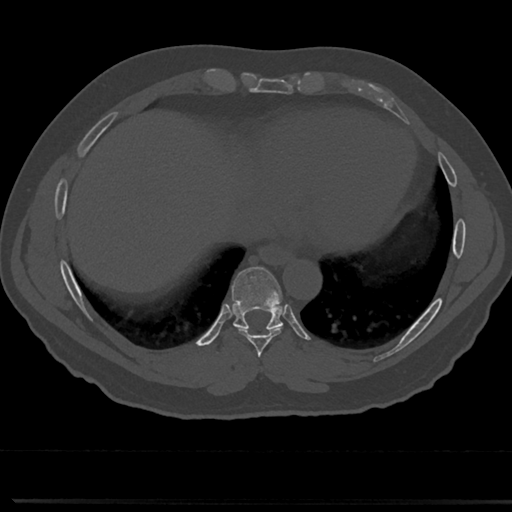
CT including the spine, one axial slice. 120 kVp. Bone window (W 1800 / L 400 HU). 0.5 mm slice thickness. 512 × 512 image matrix. Patient: male, 61 years. From the clinical record (not read from this slice): primary cancer: prostate.
Annotated regions visible in this slice (semi-automatic segmentation, software-assisted and operator-edited):
- T7 vertebra: bounding box [x1, y1, x2, y2] px = [259, 349, 266, 377]
- T8 vertebra: [211, 270, 310, 356]